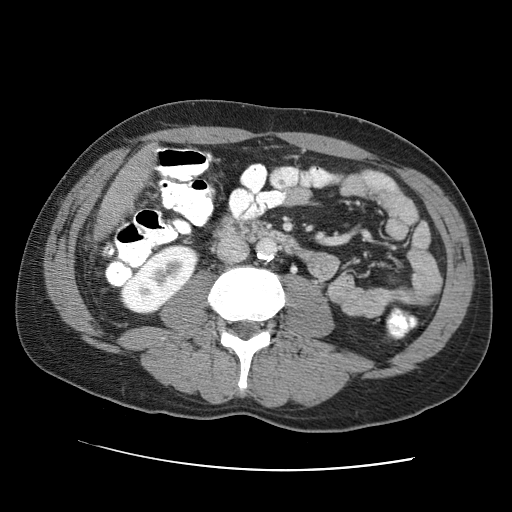
Contrast-enhanced abdominal CT (liver protocol), one axial slice; slice 7 of 95 in the series (ordered by position); one of 2 acquisitions stored at this slice position; soft-tissue window (W 400 / L 40 HU); 2.5 mm slice thickness; 512 × 512 image matrix, field of view 360 × 360 mm. Case-level facts recorded for this patient, not image findings: diagnosis: hepatocellular carcinoma (patient treated with transarterial chemoembolisation; whether this scan precedes or follows treatment is not stated here); TNM stage (as recorded): Stage-IVA; Child-Pugh class: A.
Structures marked on this image (semi-automatic segmentation, software-assisted and operator-edited):
- liver parenchyma outside the tumour (the mass and vessels are separate outlines, so this box may not span the whole liver): bounding box (x1, y1, x2, y2) in pixels: (94, 146, 155, 239)